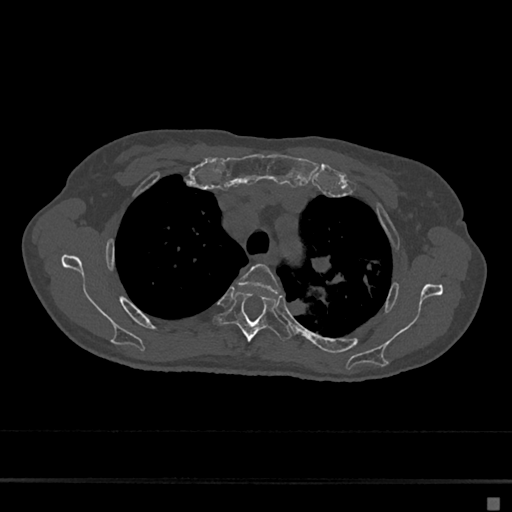
CT including the spine, one axial slice. Slice 512 of 797 in the series (ordered by position). 120 kVp. Bone window (W 1800 / L 400 HU). 0.5 mm slice thickness. 512 × 512 image matrix, field of view 360 × 360 mm. Female patient, age 68 years. From the clinical record (not read from this slice): primary cancer: renal.
Structures marked on this image (semi-automatic segmentation, software-assisted and operator-edited):
- T3 vertebra: bounding box (x1, y1, x2, y2) in pixels: (238, 264, 280, 295)
- T4 vertebra: (212, 291, 292, 342)